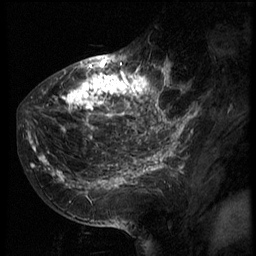
Breast MRI (dynamic contrast-enhanced), one sagittal slice. Slice 27 of 66 in the series (ordered by position). 3 images stored at this slice position (order not interpretable as contrast timing). 1.5 T. TE 4.2 ms, TR 8.9 ms. 256 × 256 image matrix, field of view 200 × 200 mm. Patient: female, 39 years. From the clinical record (not read from this slice): setting: breast cancer imaged before/during neoadjuvant chemotherapy; receptor status: HER2-positive.
Structures marked on this image (semi-automatic segmentation, software-assisted and operator-edited):
- analysis volume of interest (the breast-tissue region the enhancement analysis was run in; not a lesion): bounding box (x1, y1, x2, y2) in pixels: (29, 44, 166, 196)
- tumour enhancement mask (voxels above the 140 % enhancement threshold inside the analysis volume of interest): (29, 61, 166, 189)